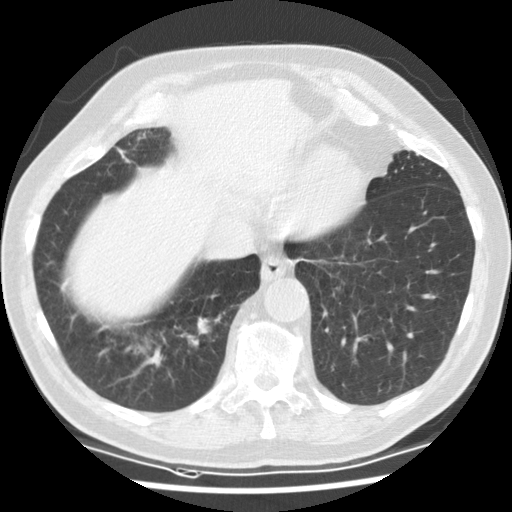
Low-dose screening chest CT, one axial slice. Slice 26 of 135 in the series (ordered by position). Reconstruction kernel STANDARD. 120 kVp. Lung window (W 1500 / L -600 HU). 2.5 mm slice thickness. 512 × 512 image matrix.
Outlined on this slice (manually delineated by an expert):
- lesion 2 (nodule, upper lobe of right lung): bounding box (x1, y1, x2, y2) in pixels: (189, 315, 221, 347)